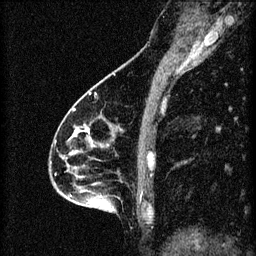
Breast MRI (dynamic contrast-enhanced), one sagittal slice. Slice 29 of 60 in the series (ordered by position). 3 images stored at this slice position (order not interpretable as contrast timing). 1.5 T. TE 4.2 ms, TR 8.2 ms. 2 mm slice thickness. 256 × 256 image matrix, field of view 180 × 180 mm. Female patient, age 46 years.
Annotated regions visible in this slice (semi-automatically segmented with operator editing):
- analysis volume of interest (the breast-tissue region the enhancement analysis was run in; not a lesion): bounding box <55,114,148,209> (left, top, right, bottom; pixels)
- tumour enhancement mask (voxels above the 70 % enhancement threshold inside the analysis volume of interest): <74,128,142,195>